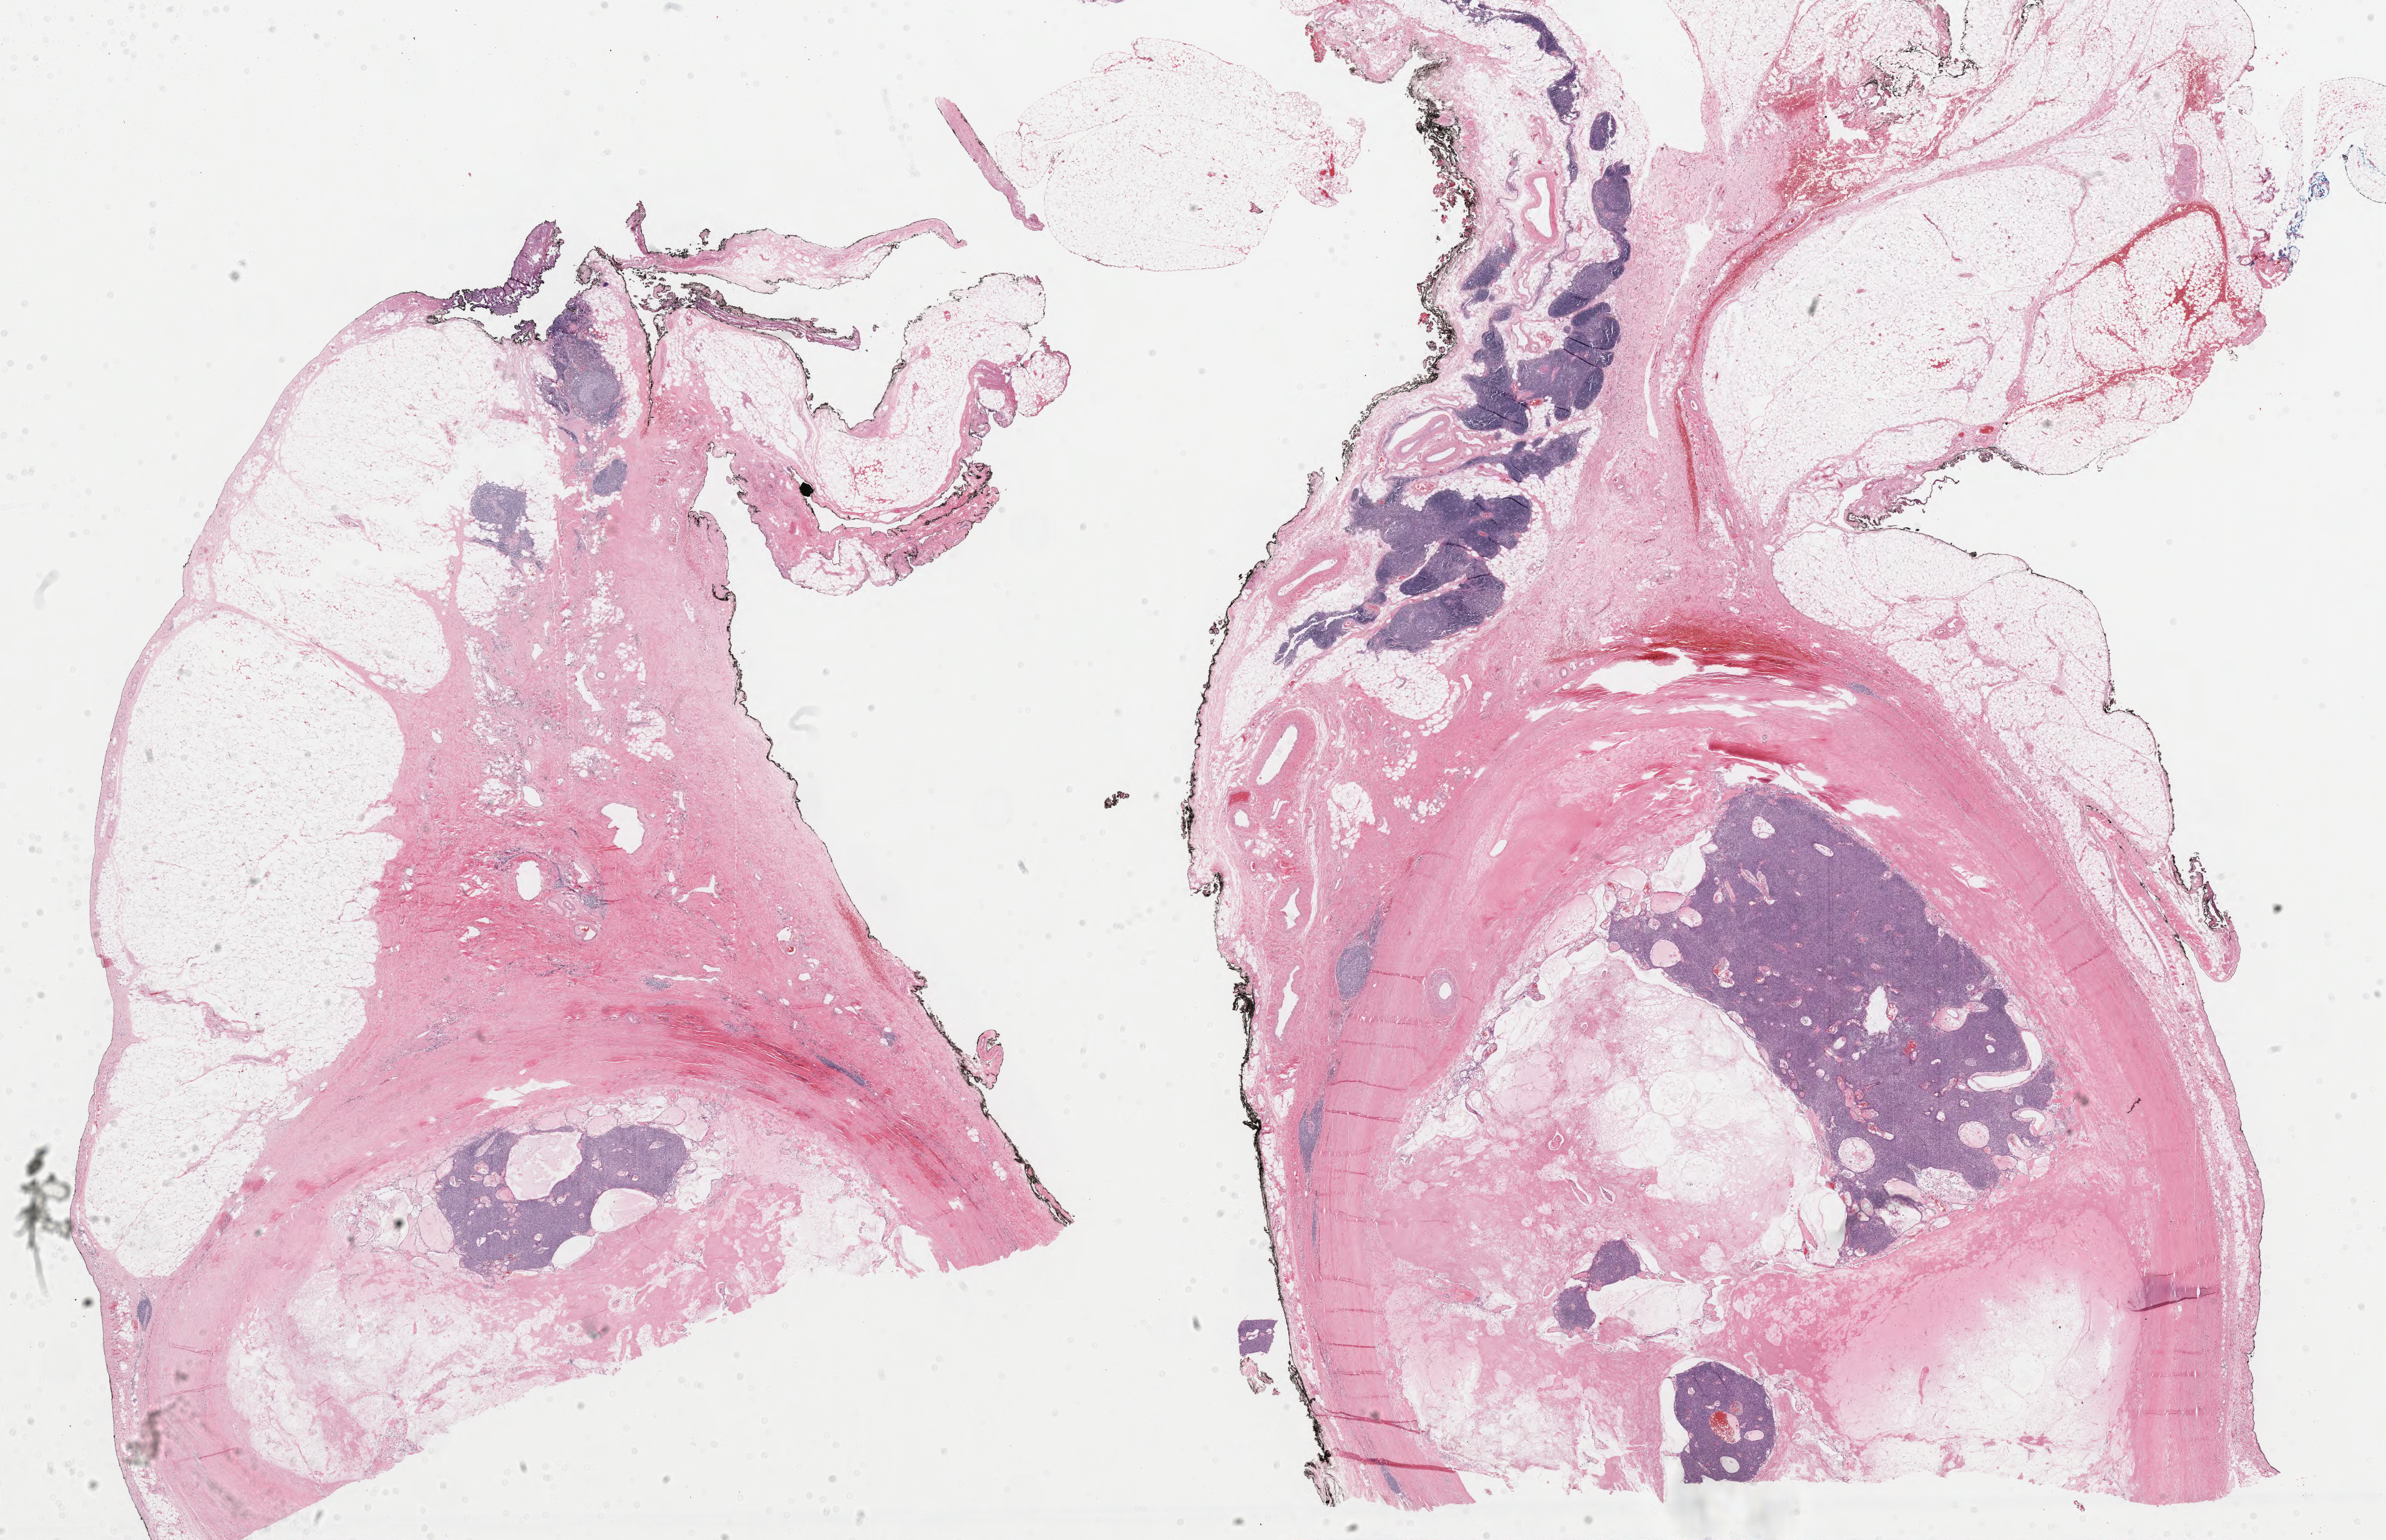
H&E whole-slide image — shown as a low-resolution overview of the whole scanned area (about 30.3 x 19.6 mm, from a 40x scan), formalin-fixed paraffin-embedded (FFPE) diagnostic section, thymus, primary tumour sample. Female patient; age at initial diagnosis 43 years.
* histologic diagnosis: Thymoma, type B2, malignant